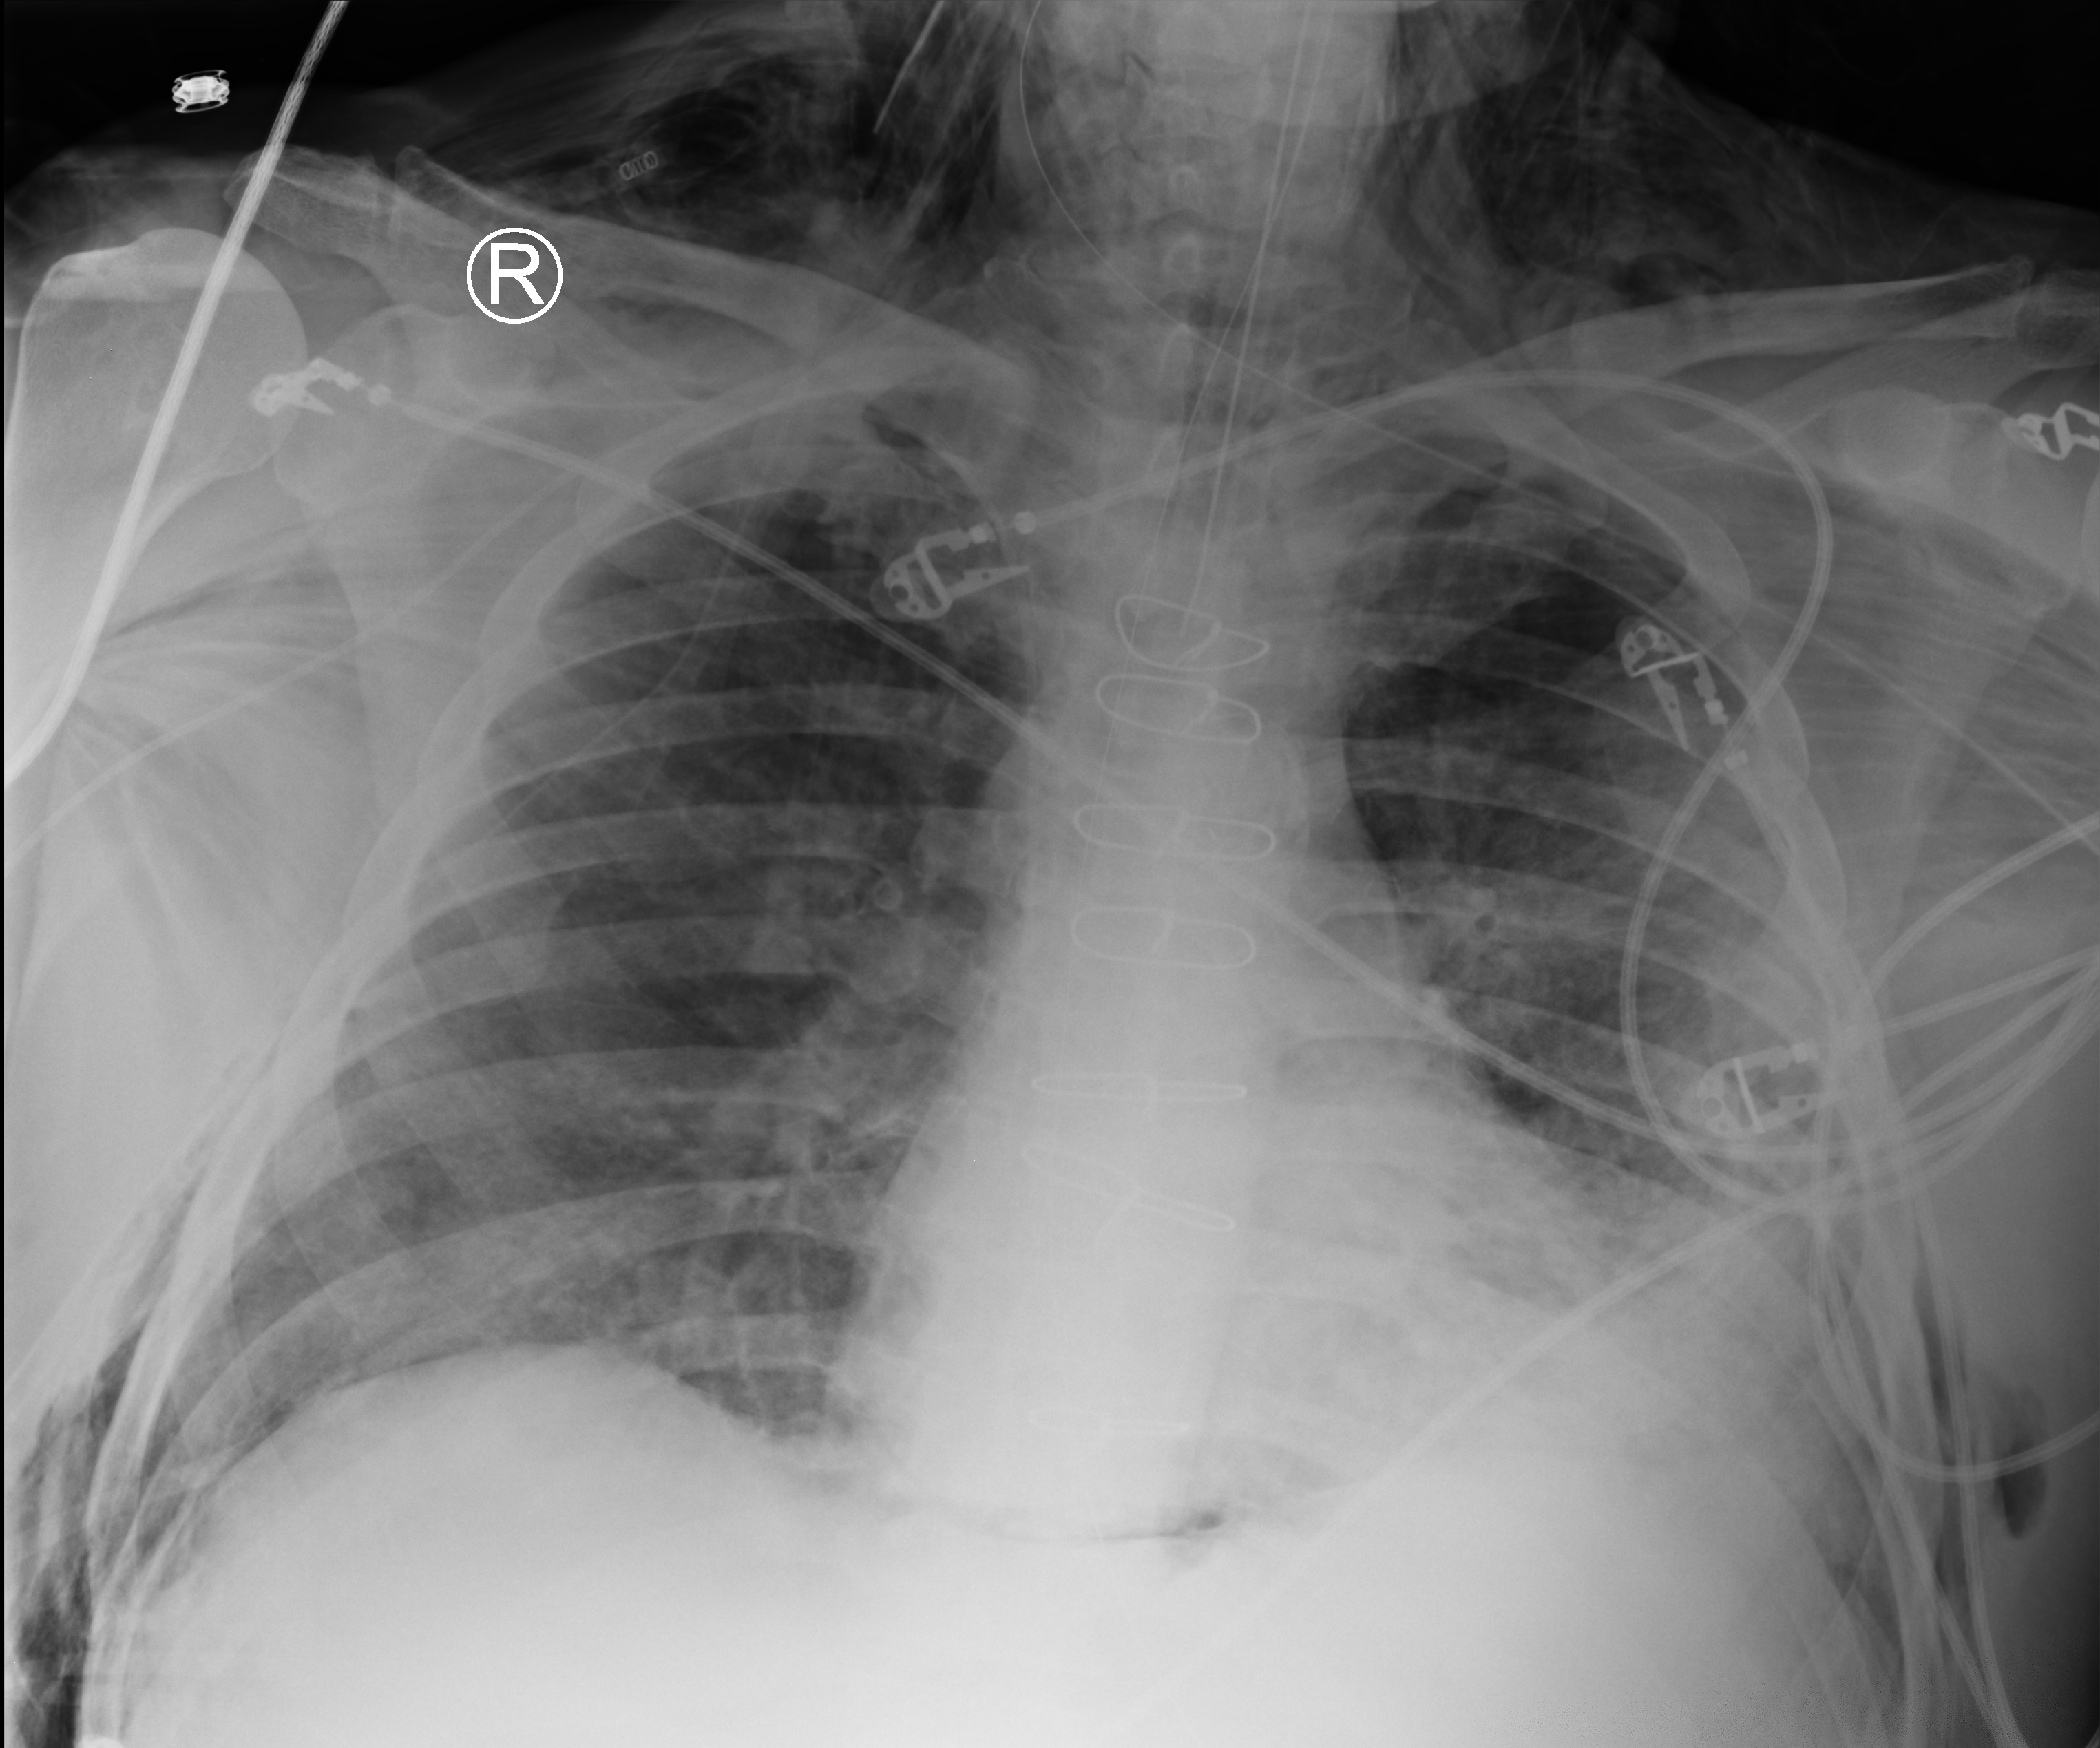
Bedside chest radiograph (computed radiography). Patient hospitalised with COVID-19; male, aged 60–74 years.
From the hospital-stay record, not from the radiograph (when in the stay this image was taken is not recorded): other chronic lung disease (admission record): no; admitted to intensive care during this hospital stay: yes.